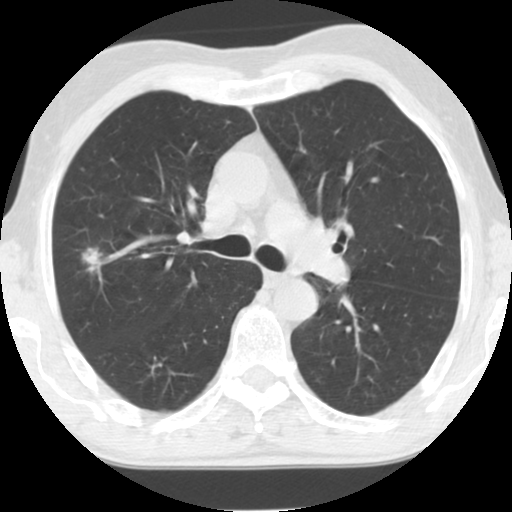
Low-dose screening chest CT, one axial slice; slice 82 of 124 in the series (ordered by position); reconstruction kernel STANDARD; 120 kVp; lung window (W 1500 / L -600 HU); 2.5 mm slice thickness; 512 × 512 image matrix, field of view 310 × 310 mm.
Annotated regions visible in this slice (expert manual segmentation):
- lesion 1 (tumor, upper lobe of right lung): box from (x=82, y=248) to (x=105, y=273) px